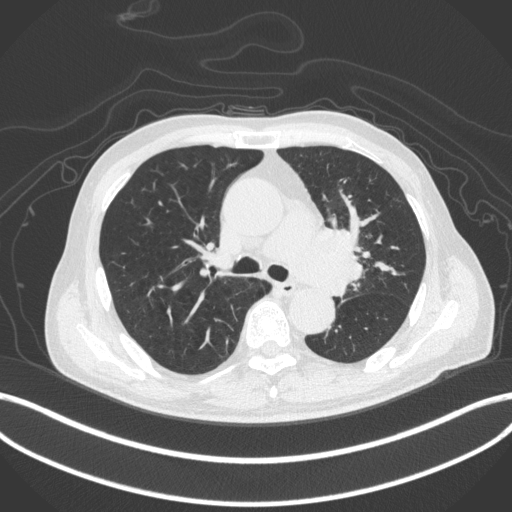
Chest CT, one axial slice; position 277 of 420 along the scan axis; 120 kVp; lung window (W 1500 / L -600 HU); 512 × 512 image matrix, field of view 400 × 400 mm. Male patient, age 77 years. Case-level facts recorded for this patient, not image findings: clinical TNM (as recorded): T3 N1 M0.
Annotated regions visible in this slice (rectangle marked by the reading radiologist):
- lung tumour (recorded histology: adenocarcinoma): bounding box <294,218,360,290> (left, top, right, bottom; pixels)